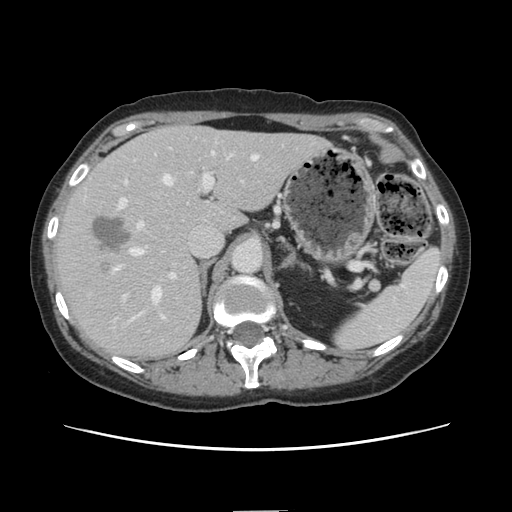
Contrast-enhanced abdominal CT, one axial slice; slice 93 of 141 in the series (ordered by position); soft-tissue window (W 400 / L 40 HU); 2.5 mm slice thickness; 512 × 512 image matrix, field of view 350 × 350 mm. Female patient, age 63 years. Case-level facts recorded for this patient, not image findings: diagnosis: colorectal cancer liver metastases, imaged before liver resection; multiple liver metastases: yes; largest metastasis: 3.2 cm.
Outlined on this slice (manually delineated by an expert):
- hepatic veins: bounding box <115,153,257,320> (left, top, right, bottom; pixels)
- liver: <56,127,327,359>
- planned liver remnant (the part of the liver to remain after resection): <181,127,327,233>
- portal vein (with intrahepatic branches): <117,149,237,298>